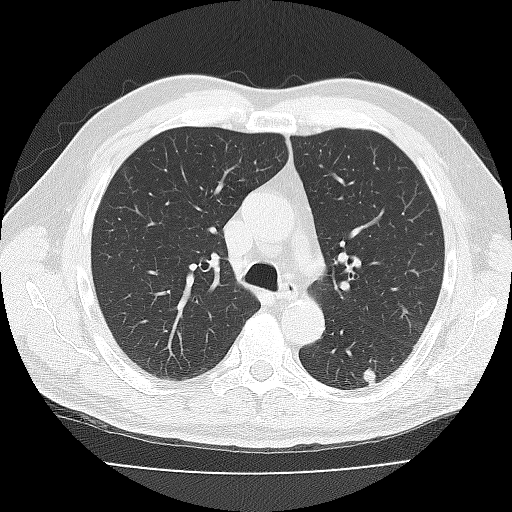
Axial slice from a low-dose chest CT screening exam; second annual screen; lung window (W 1500 / L -600 HU); 3 mm slice thickness; reconstruction kernel FC30 (as recorded); slice 33 of 96 in the series. Male participant, aged 65 years at enrolment.
Lesion marked by an expert reader, bounding box [x1, y1, x2, y2] px = [351, 357, 393, 394]. Screening reader's record for this exam (one nodule recorded; not confirmed to be the boxed lesion): non-calcified nodule or mass ≥4 mm, left lower lobe, 11 × 10 mm, smooth margins, soft tissue attenuation, pre-existing on the prior screen: yes; interval growth: yes. Official screen result: positive, other. Later outcome: lung cancer diagnosed 8 days after this screen — adenocarcinoma, NOS, left lower lobe, well differentiated (G1), stage IB (AJCC 6th edition), 10 mm at pathology.